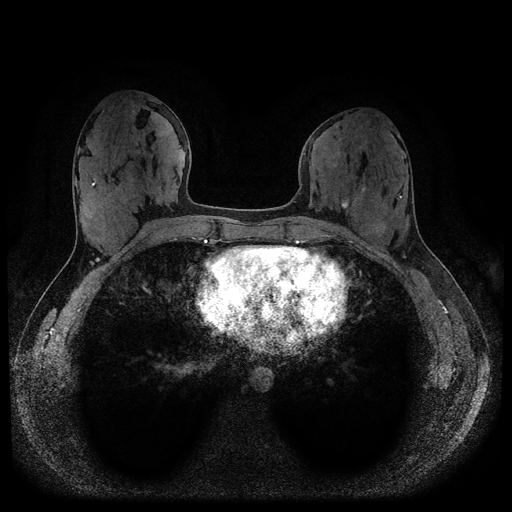
Breast MRI (dynamic contrast-enhanced, multi-phase), one axial slice. Position 42 of 116 along the scan axis. Dynamic contrast-enhanced series, time point 2 of 5 at this slice position (early post-contrast). 1.5 T. TE 2.6 ms, TR 5.3 ms. 512 × 512 image matrix. Patient: female, 33 years.
Structures marked on this image (semi-automatically segmented with operator editing):
- breast lesion (labelled benign in the annotation): bounding box [x1, y1, x2, y2] px = [340, 199, 349, 210]